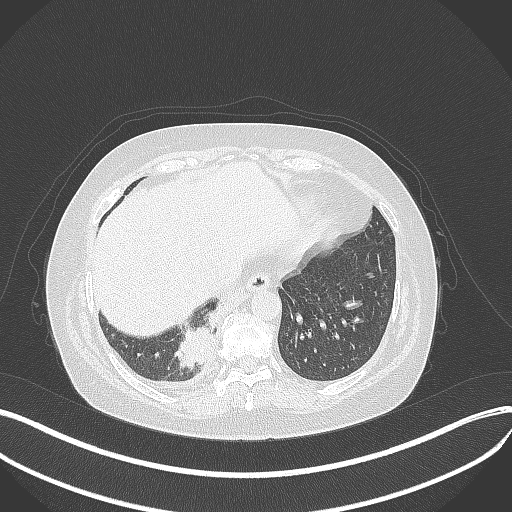
Chest CT, one axial slice; slice 91 of 381 in the series (ordered by position); reconstruction kernel B70f; 120 kVp; lung window (W 1500 / L -600 HU); 1 mm slice thickness; 512 × 512 image matrix, field of view 400 × 400 mm. Female patient, age 56 years. From the clinical record (not read from this slice): clinical TNM (as recorded): T2b N1 M0; histopathological grade: G3.
Annotated regions visible in this slice (bounding box drawn by a radiologist):
- lung tumour (recorded histology: small cell carcinoma): bounding box [x1, y1, x2, y2] px = [170, 305, 226, 374]